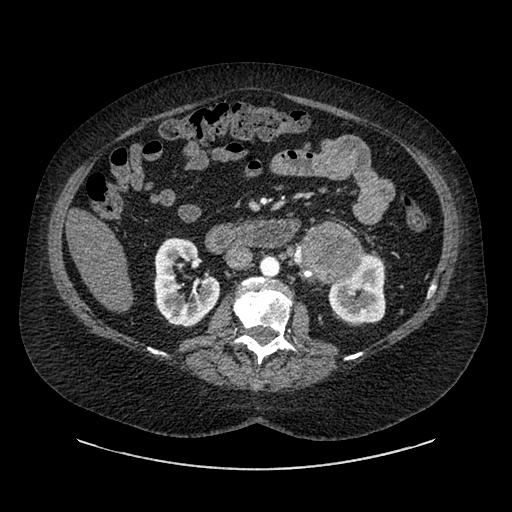
Contrast-enhanced abdominal CT, one axial slice. Position 502 of 769 along the scan axis. Reconstruction kernel SOFT. Intravenous contrast given. Soft-tissue window (W 400 / L 40 HU). 0.62 mm slice thickness. 512 × 512 image matrix, field of view 460 × 460 mm. Female patient, age 61 years. Case-level facts recorded for this patient, not image findings: diagnosis: adrenocortical carcinoma; tumour side: left adrenal; tumour size at pathology: 13 cm; Ki-67 index: 79 %; stage (as recorded): 2.
Annotated regions visible in this slice (semi-automatically segmented with operator editing):
- mass: bounding box [x1, y1, x2, y2] px = [305, 226, 362, 280]